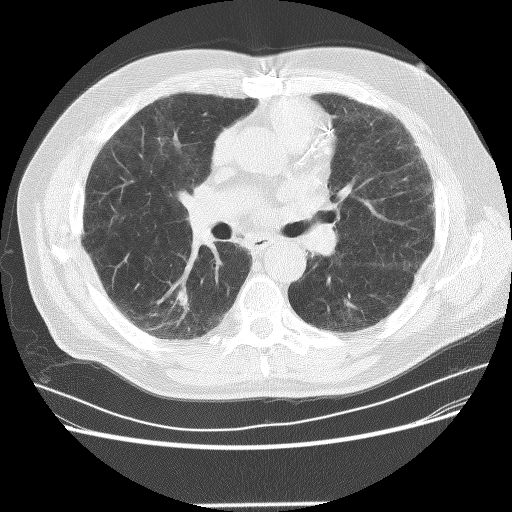
Chest CT (low-dose screening protocol), one axial image, baseline screening round, lung window (W 1500 / L -600 HU), 2.5 mm slice thickness, lung (sharp) reconstruction kernel (BONE), 120 kVp, 512 × 512 image matrix. Male, age 72 years at enrolment. Former smoker at enrolment.
• Lesion marked by an expert reader, bounding box (x1, y1, x2, y2) in pixels: (159, 281, 200, 322).
• The screening reader recorded 2 non-calcified nodules or masses ≥4 mm on this exam (right lower lobe, left lower lobe); which of them this box marks is not recorded.
• Participant outcome: lung cancer diagnosed 436 days after this screen (after the second annual screen) — squamous cell carcinoma, NOS, right lower lobe, poorly differentiated (G3), stage IB (AJCC 6th edition), 42 mm at pathology.